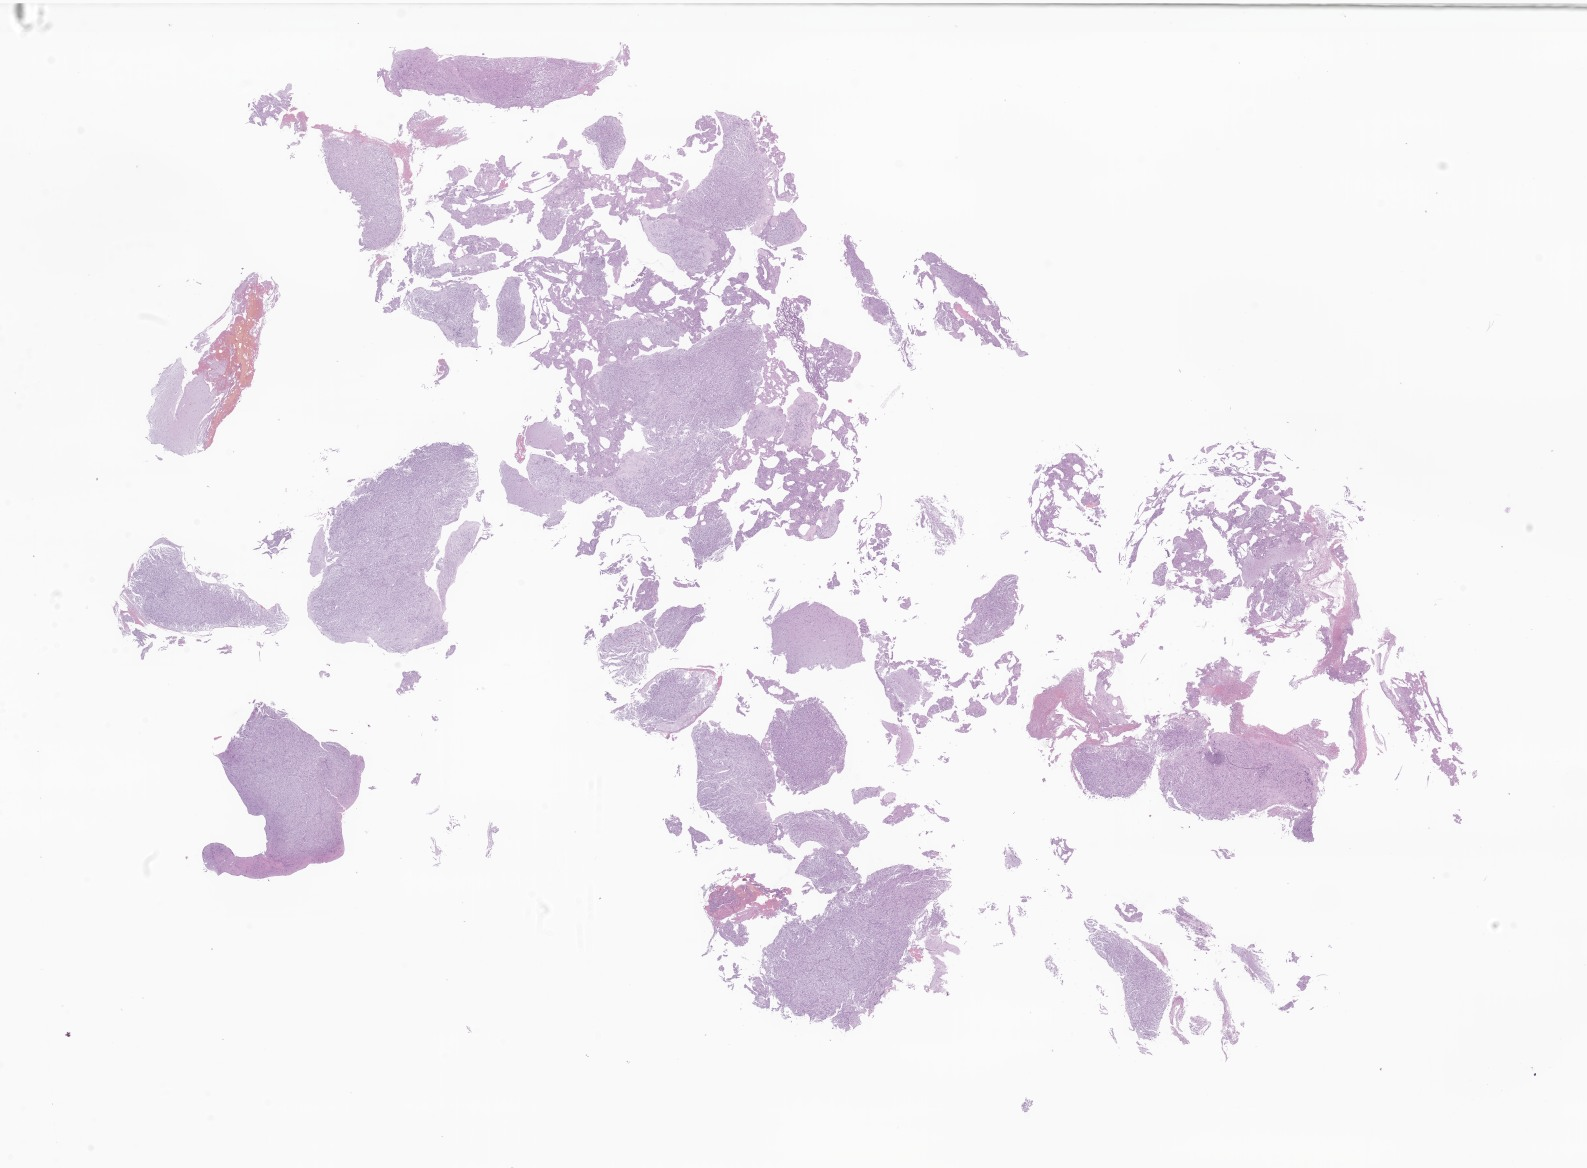
Hematoxylin and eosin (H&E) whole-slide image of tumor tissue from the frontal lobe, shown as a low-resolution overview of the whole scanned area (about 26.8 x 19.7 mm). Formalin-fixed, paraffin-embedded (FFPE) tissue. Patient: female, age 149 months (12 years 5 months).
Recorded diagnosis: Pleomorphic xanthoastrocytoma, NOS.